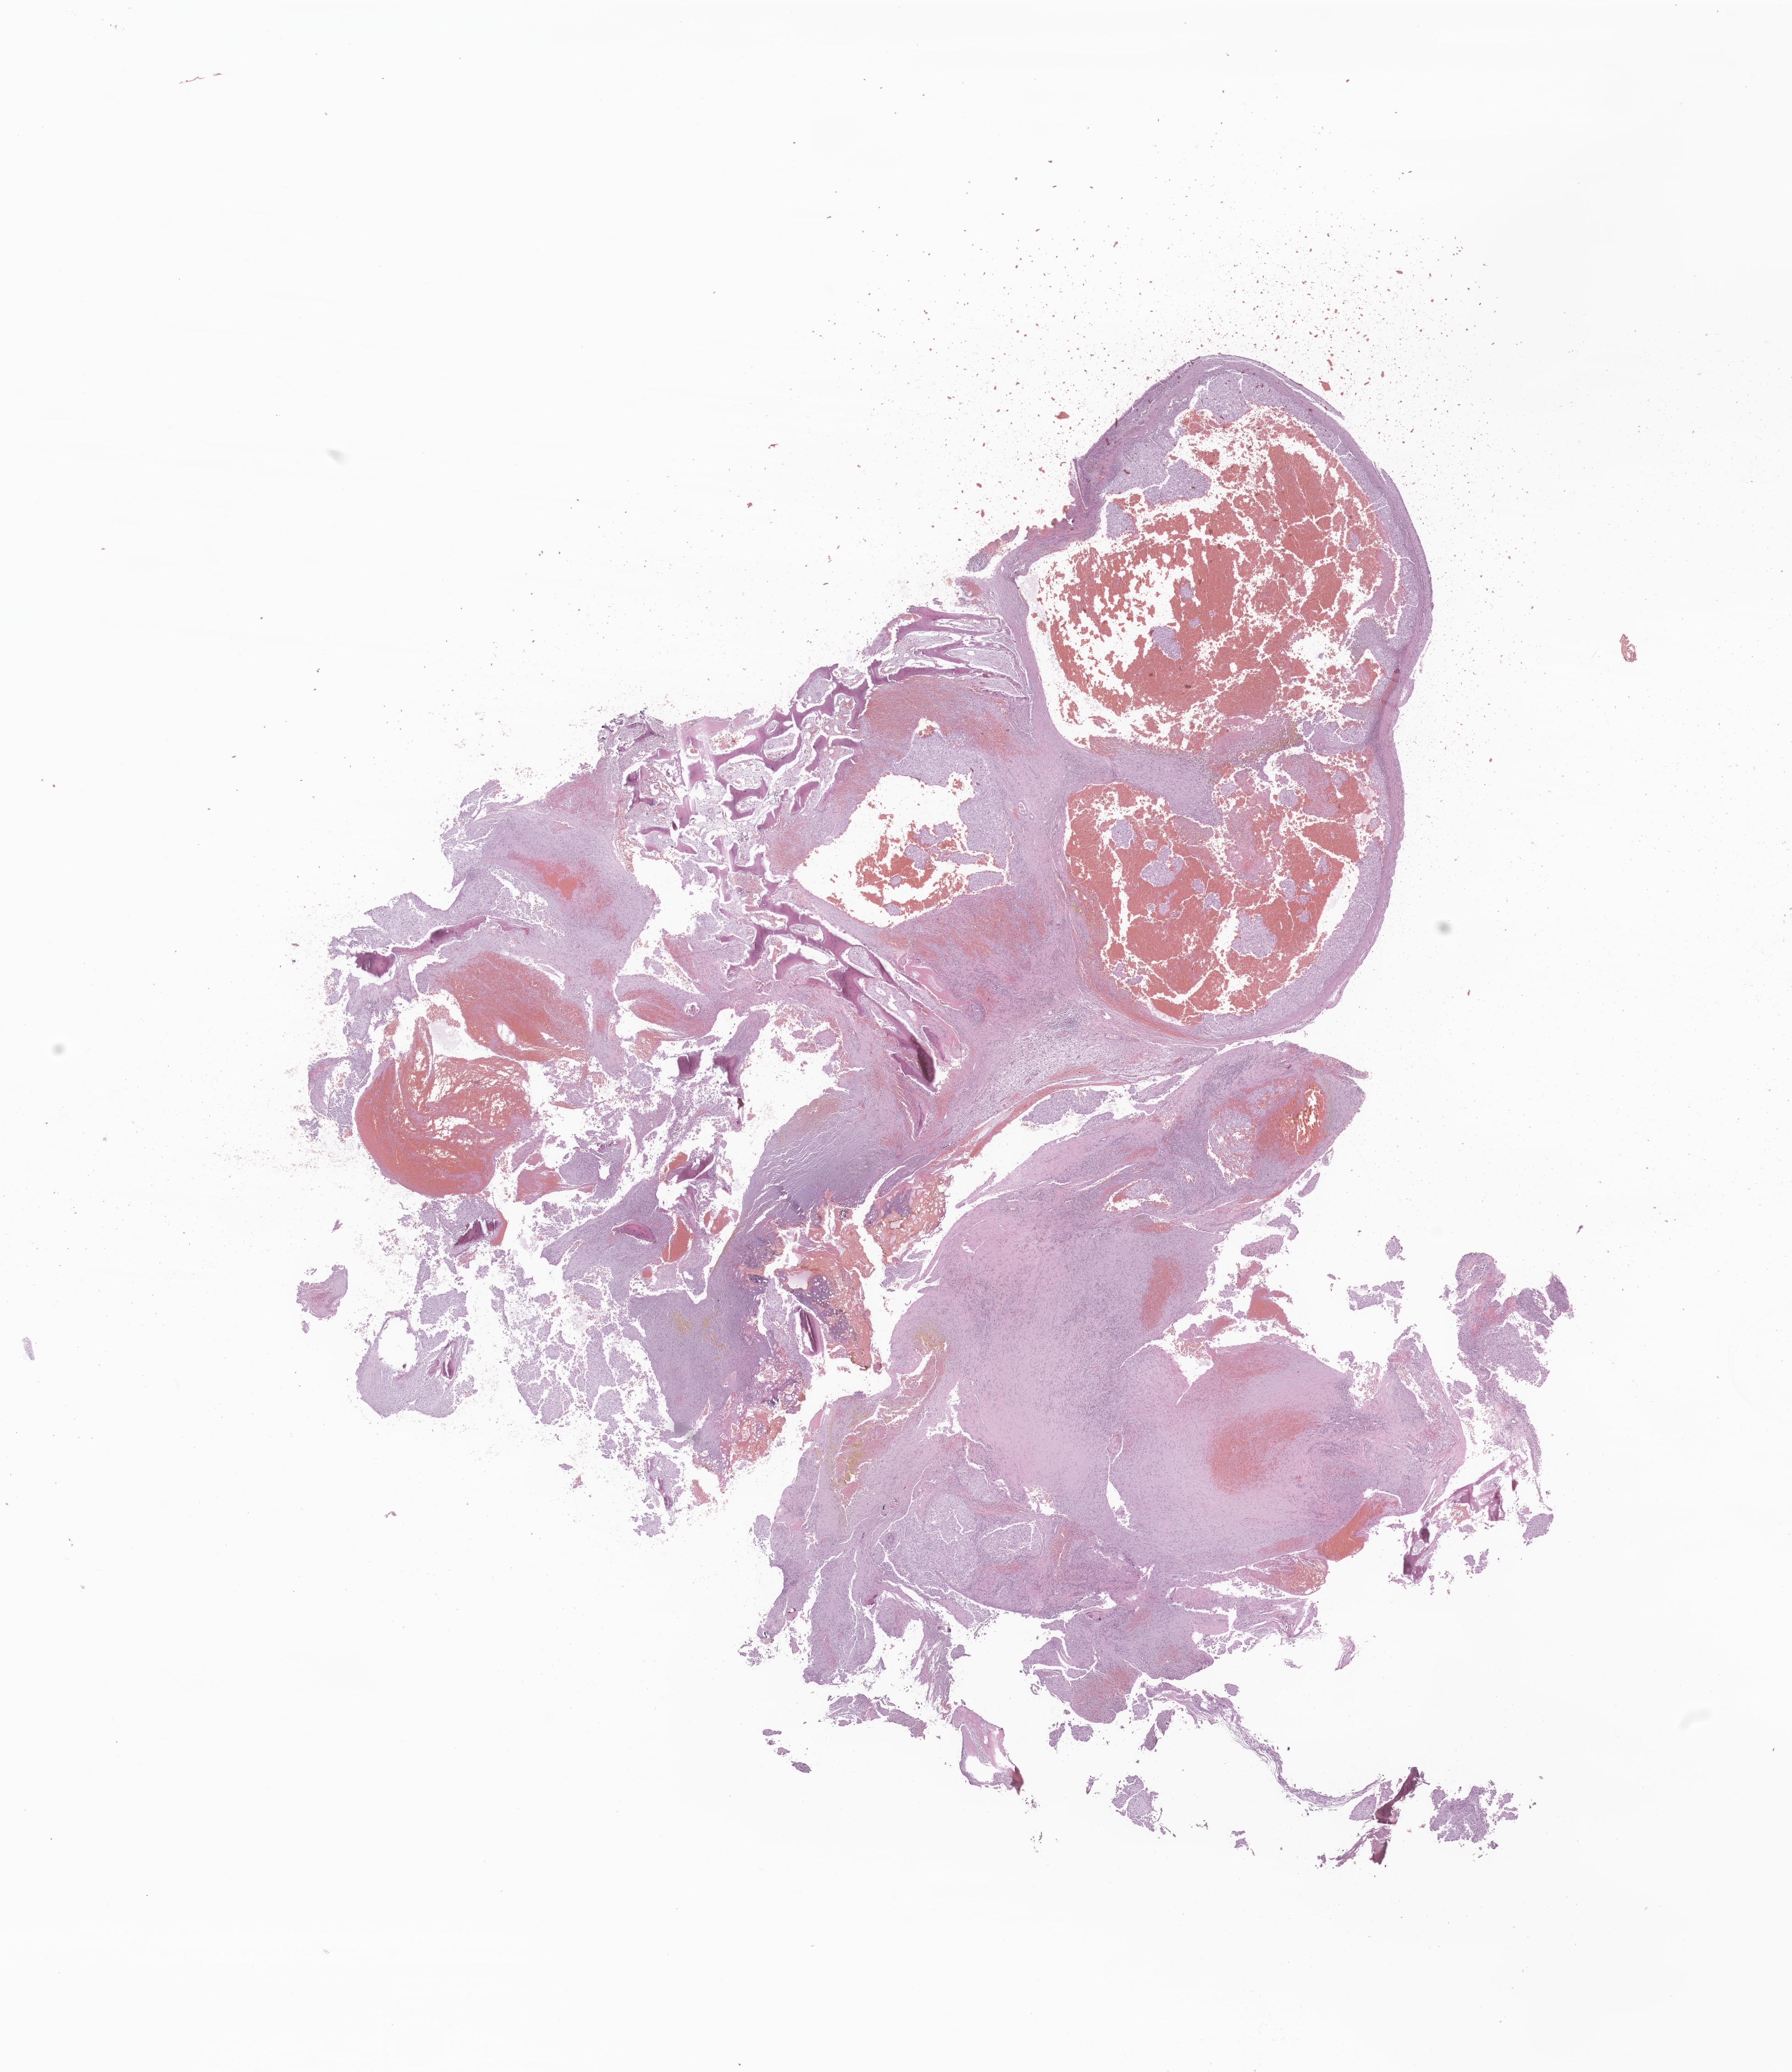
Hematoxylin and eosin (H&E) whole-slide image of tumor tissue from the brain — low-resolution overview of the scanned area, about 16.5 x 19.0 mm. Formalin-fixed paraffin-embedded section. Patient male; age 85 months (7 years 1 month).
Diagnosis: Chordoma, NOS.